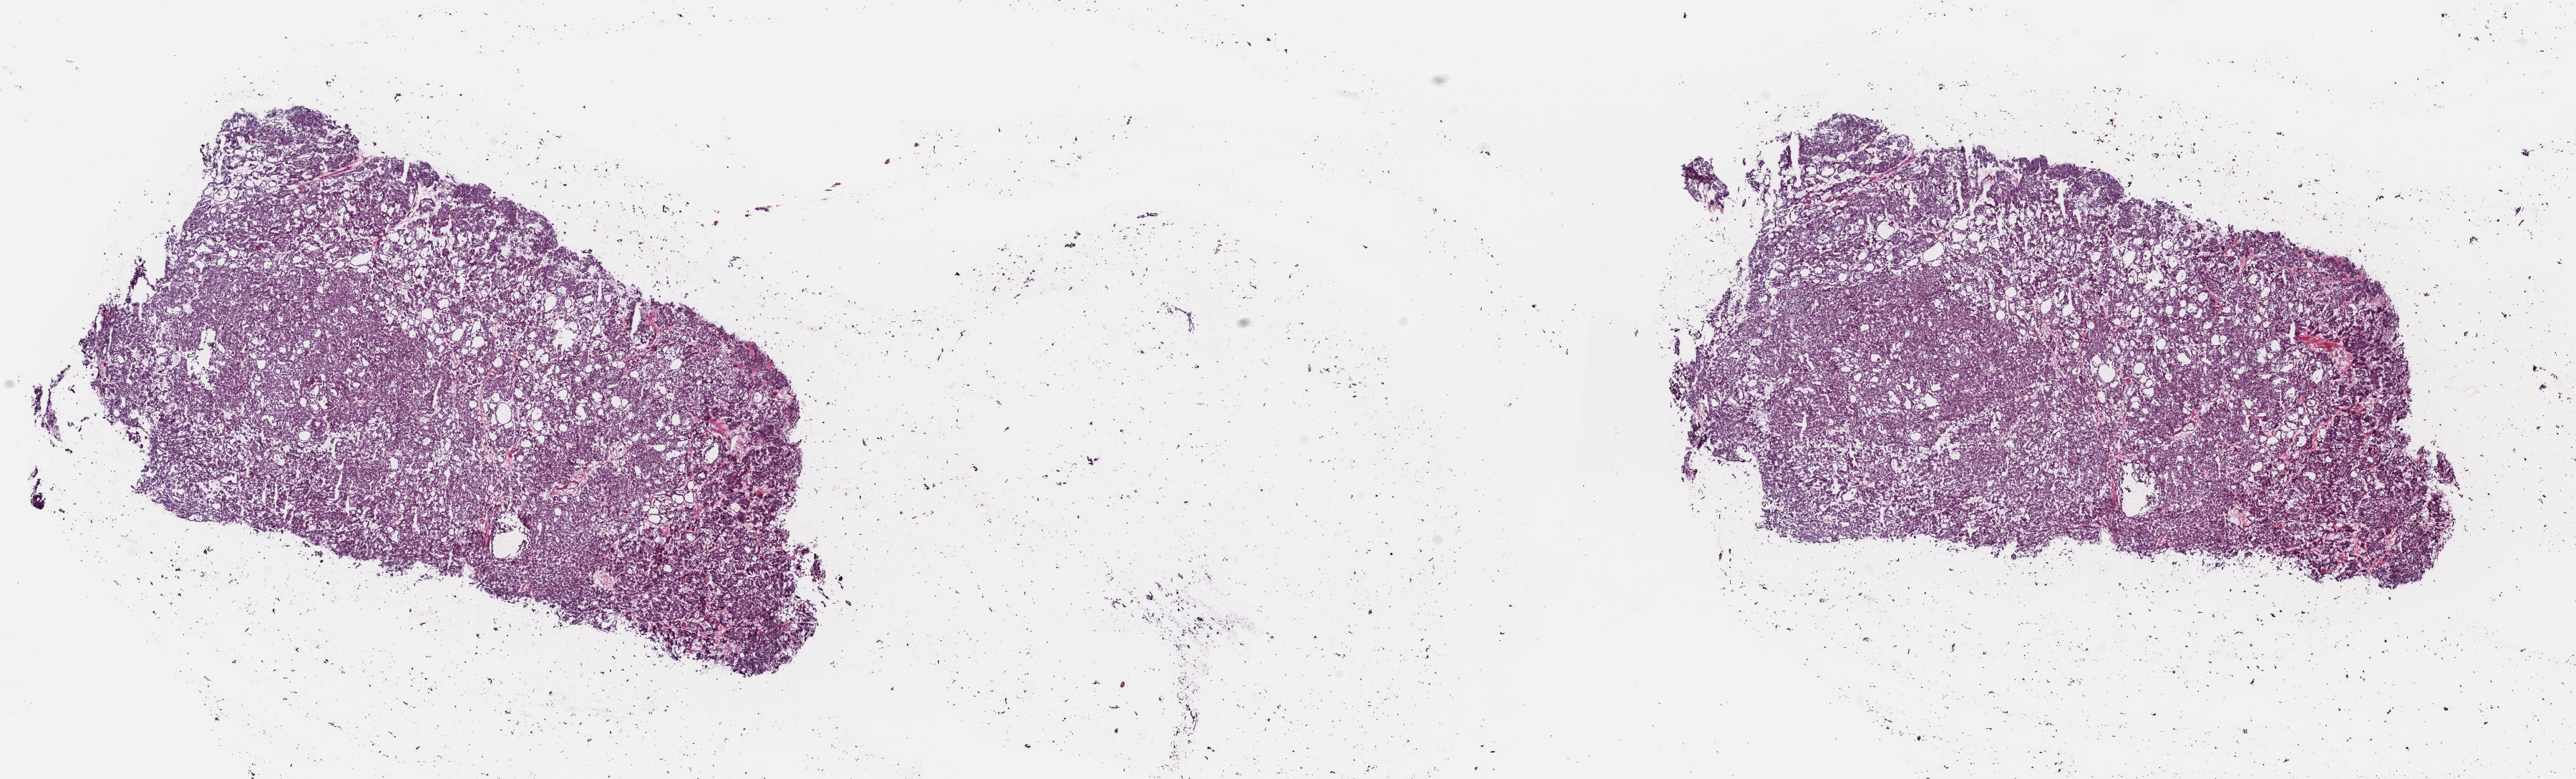
H&E whole-slide image, a low-resolution overview of the entire scanned area, about 28.4 x 8.6 mm (slide scanned at 40x). Frozen section from the top of the tissue portion. Thyroid, primary tumour sample. Male, age 62 years at initial diagnosis. Slide review estimates, as recorded: tumour cells 100%, tumour nuclei 95%, normal cells 0%, stromal cells 0%, necrosis 0%. Infiltration values recorded for this section: lymphocyte infiltration 0%, monocyte infiltration 0%, neutrophil infiltration 0%.
• histologic diagnosis: Papillary carcinoma, follicular variant (thyroid gland)
• lymph nodes positive (case pathology): 0 of 5 examined
• AJCC pathologic stage: I